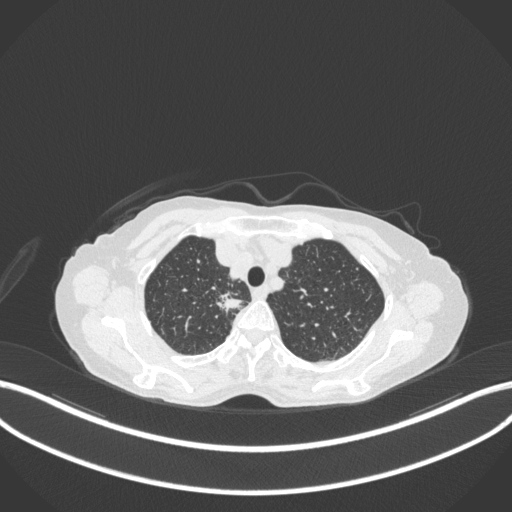
Chest CT, one axial slice; position 308 of 363 along the scan axis; lung window (W 1500 / L -600 HU); 1 mm slice thickness; 512 × 512 image matrix, field of view 400 × 400 mm. Female patient, age 75 years. Case-level facts recorded for this patient, not image findings: clinical TNM (as recorded): T1c N1 M1.
Outlined on this slice (bounding box drawn by a radiologist):
- lung tumour (recorded histology: adenocarcinoma): bounding box (x1, y1, x2, y2) in pixels: (215, 289, 247, 316)